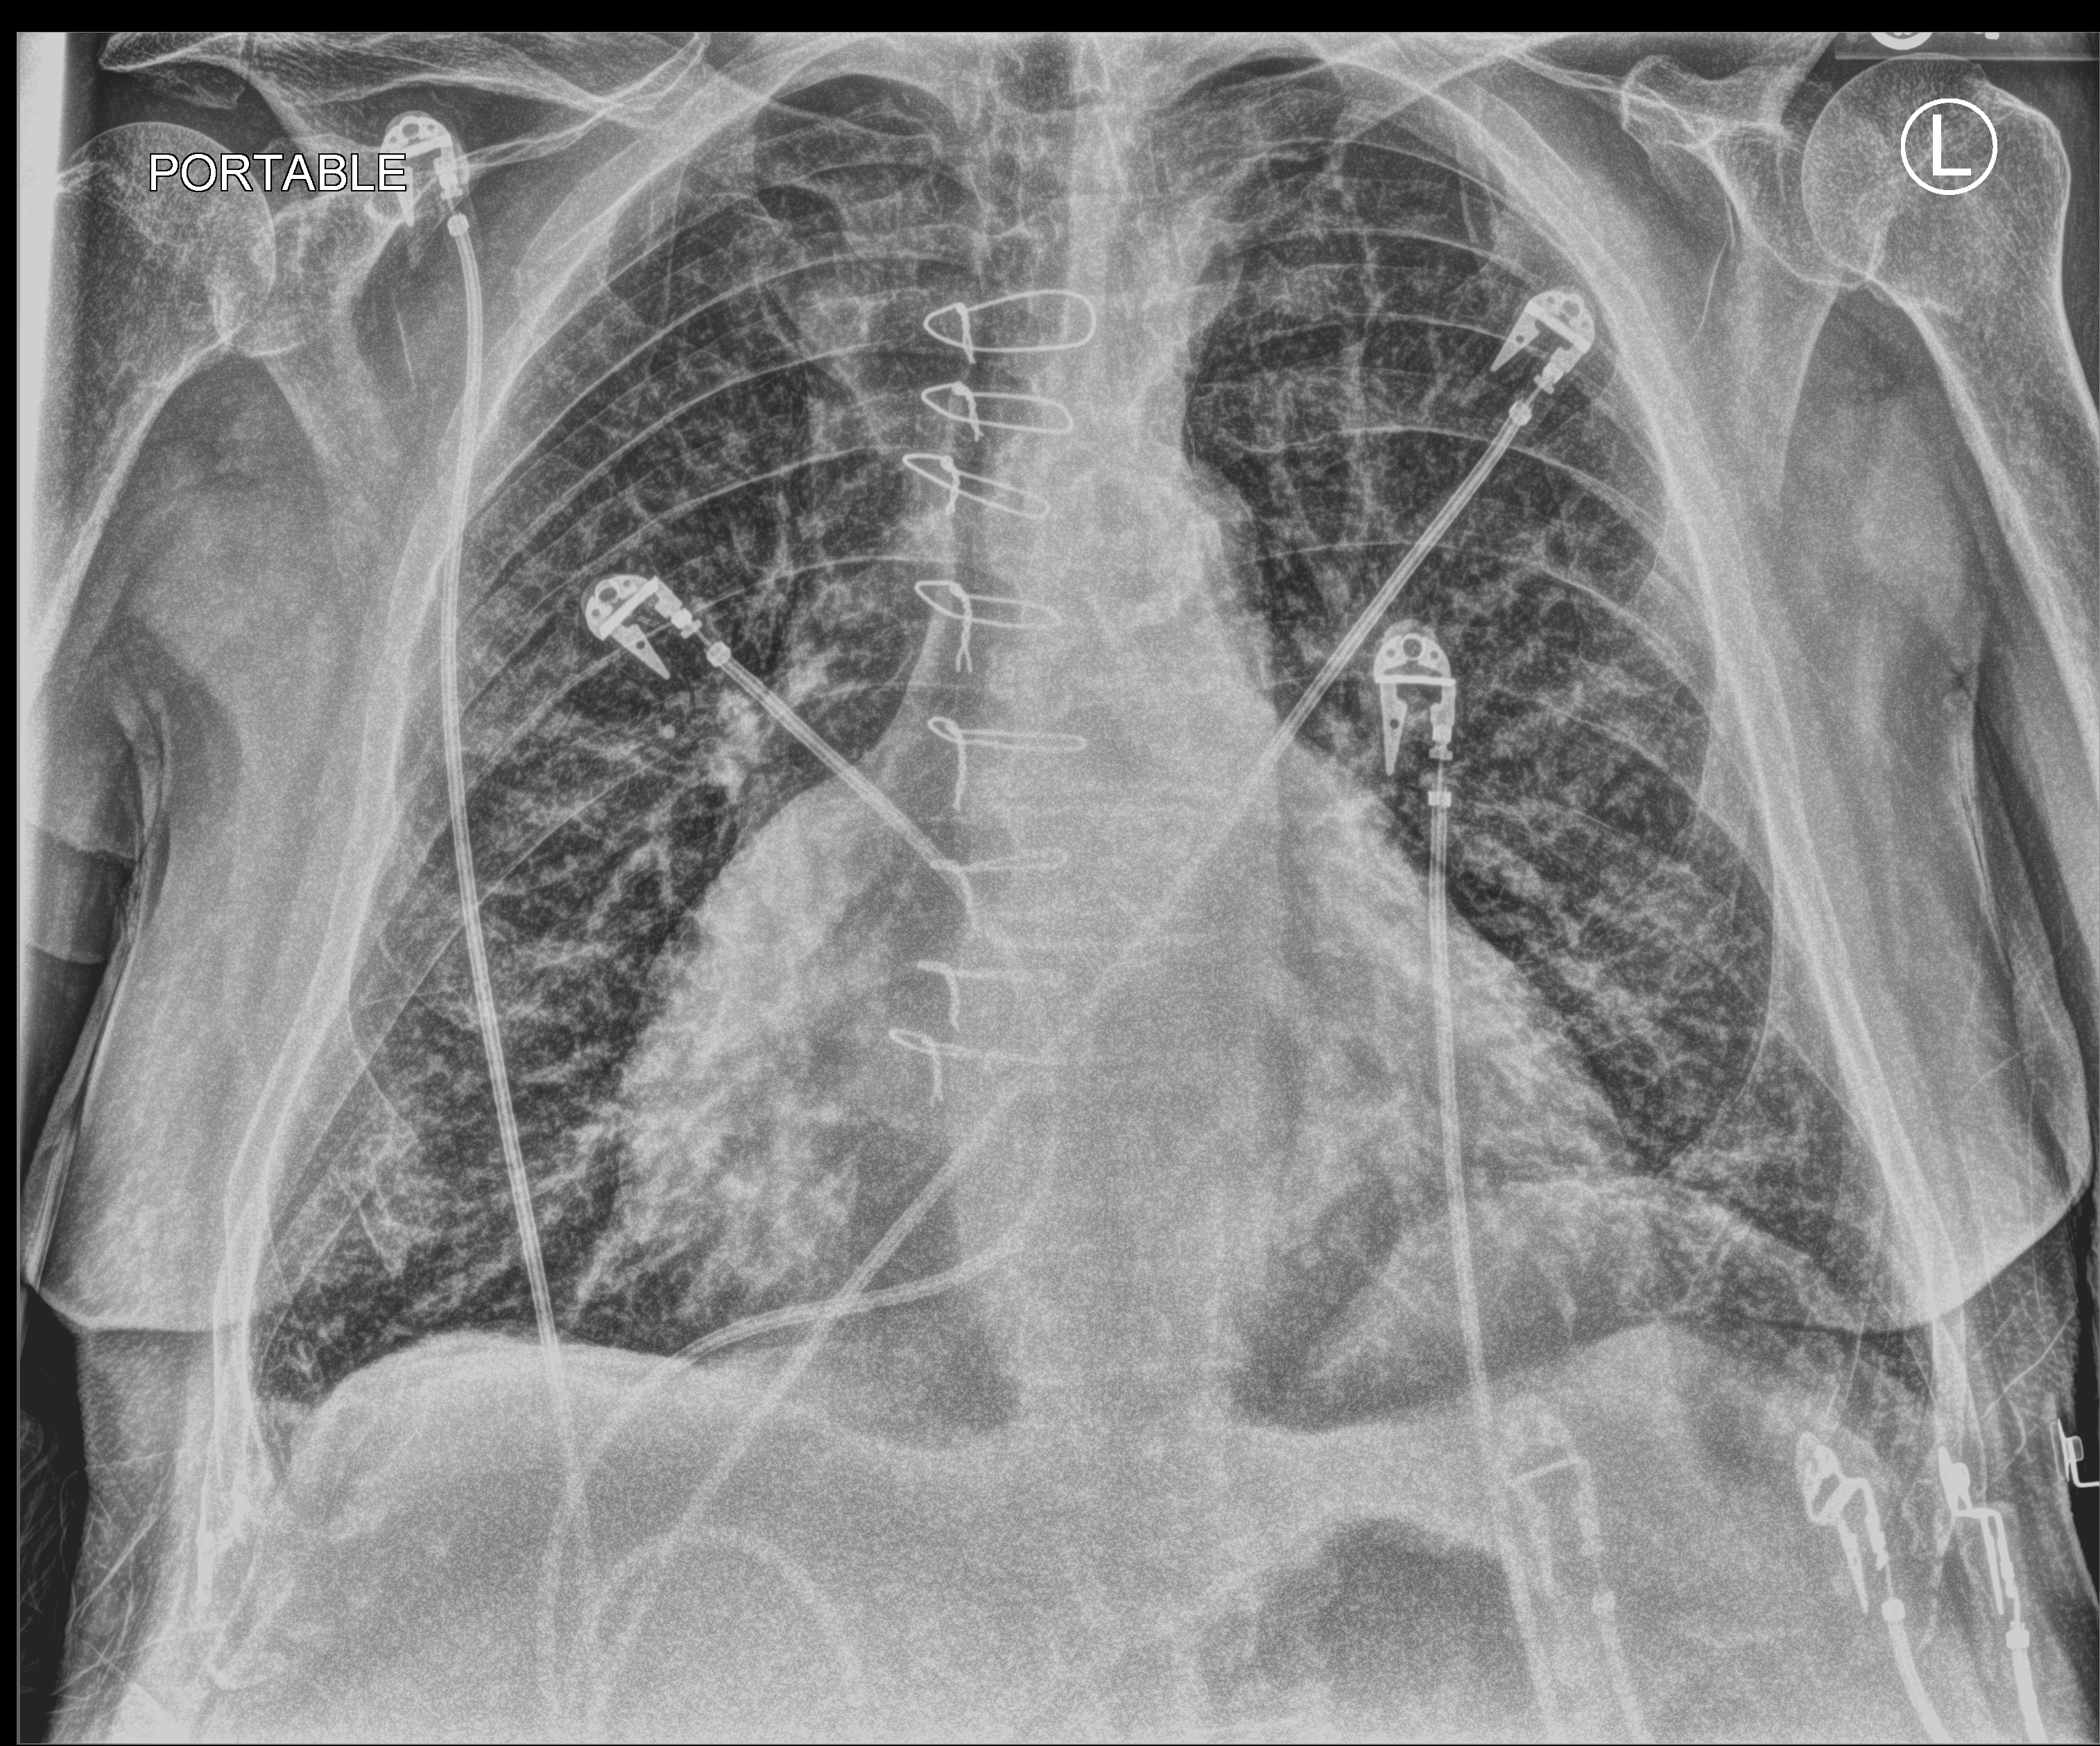
Chest X-ray (portable), anteroposterior (AP) projection. Patient hospitalised with COVID-19; male, aged 75–90 years.
Hospital-stay facts (about this admission, not read from this image; timing relative to this image not recorded): admitted to intensive care during this hospital stay: yes.